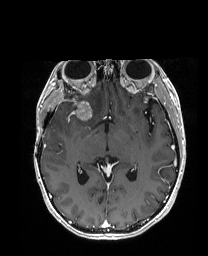
Brain MRI from a brain-tumour surgery series, one axial slice. Position 100 of 192 along the scan axis. T1-weighted post-contrast. 1 mm slice thickness. 208 × 256 image matrix, field of view 203 × 250 mm. From the clinical record (not read from this slice): histopathology: Metastatic Carcinoma from Breast primary.
Outlined on this slice (manually delineated by an expert):
- tumour: box from (x=55, y=98) to (x=104, y=119) px